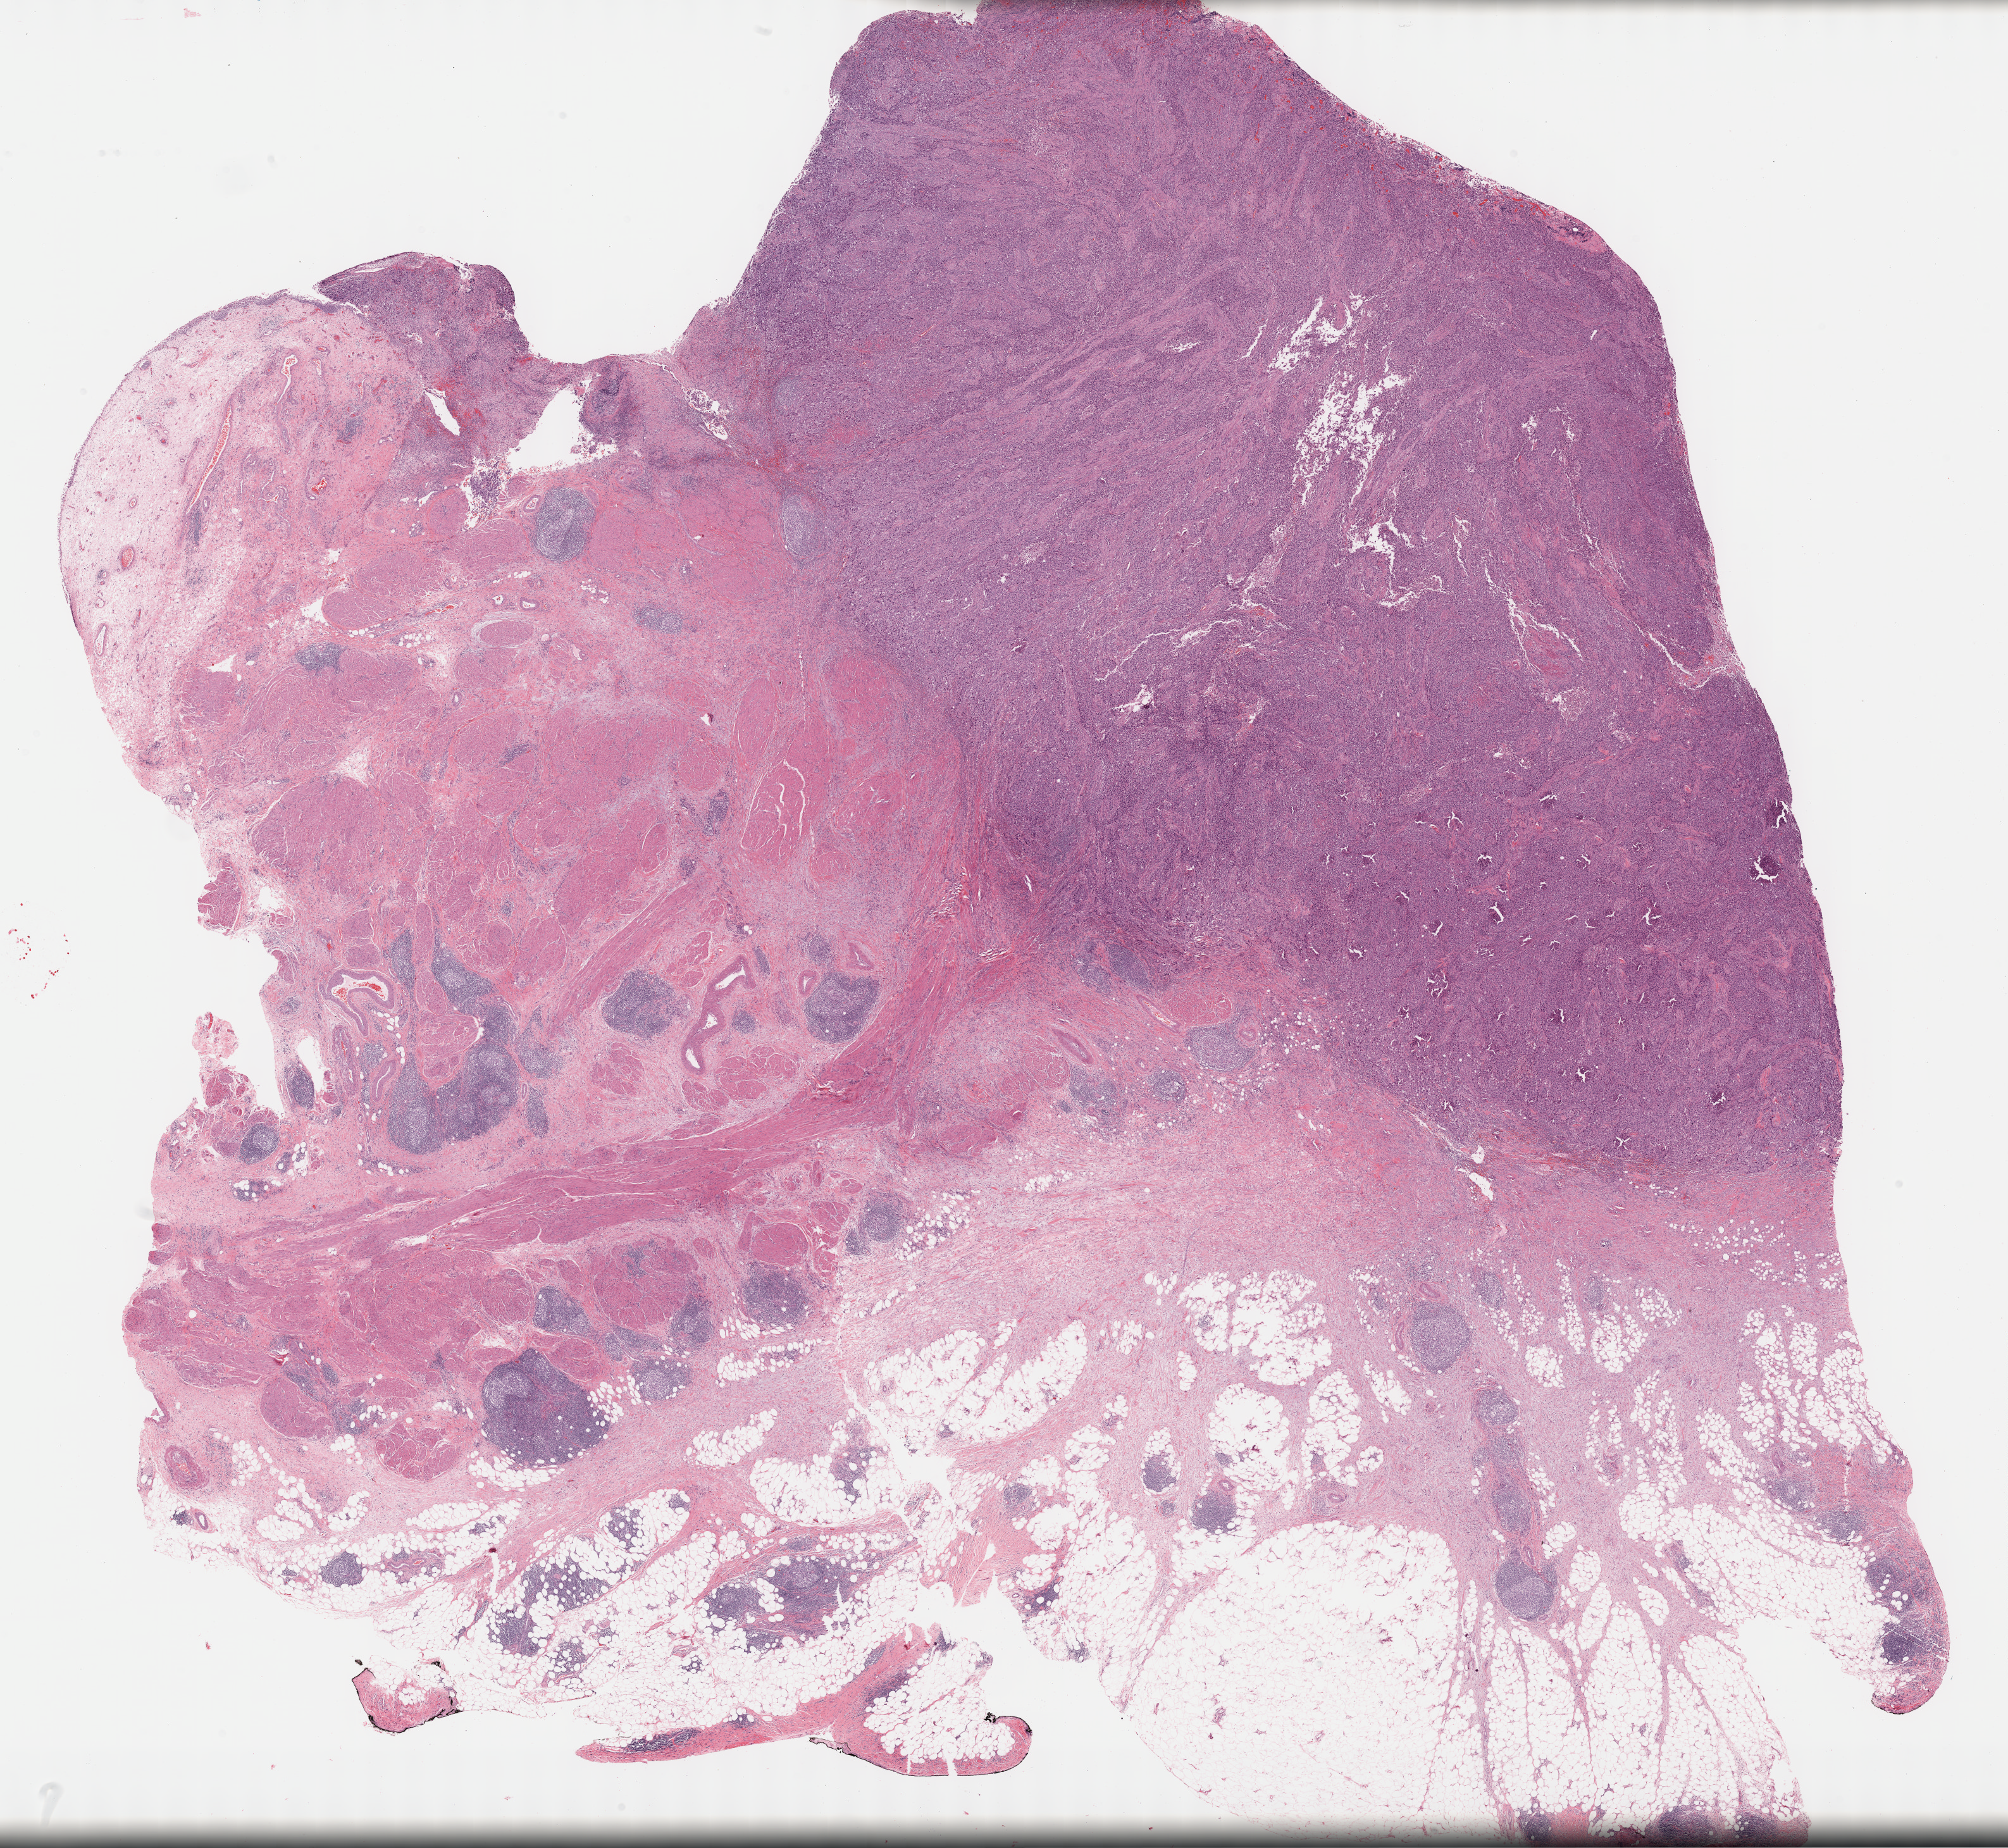
Whole-slide histology image, H&E — low-resolution overview of the scanned area, about 25.7 x 23.6 mm; formalin-fixed paraffin-embedded (FFPE) diagnostic section; primary tumour sample from the bladder. Female, age 67 years at initial diagnosis. Histologic grade: high grade.
Lymph nodes positive (case pathology): 0 of 29 examined. AJCC pathologic stage: III (5th edition). Diagnosis: Transitional cell carcinoma (dome of bladder).